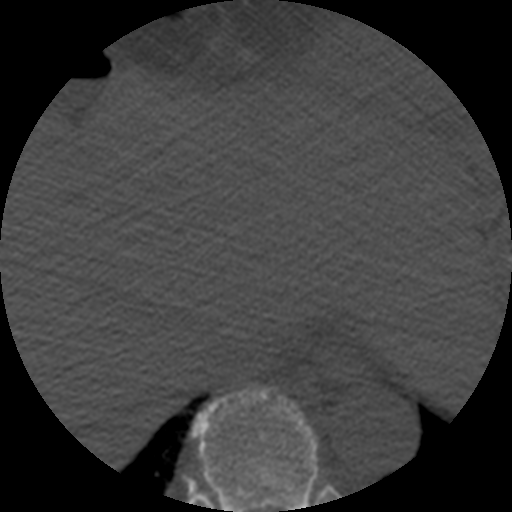
CT including the spine, one axial slice; slice 295 of 508 in the series (ordered by position); reconstruction kernel STANDARD; 120 kVp; bone window (W 1800 / L 400 HU); 1.25 mm slice thickness; 512 × 512 image matrix, field of view 160 × 160 mm. Patient age 57 years. Case-level facts recorded for this patient, not image findings: primary cancer: prostate.
Structures marked on this image (semi-automatic segmentation, software-assisted and operator-edited):
- T9 vertebra: bounding box [x1, y1, x2, y2] px = [192, 390, 318, 512]